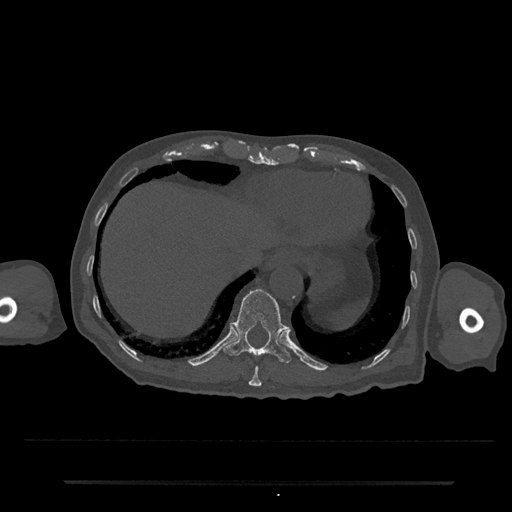
CT including the spine, one axial slice. Slice 265 of 797 in the series (ordered by position). Reconstruction kernel Br40s/3. 120 kVp. Bone window (W 1800 / L 400 HU). 0.5 mm slice thickness. 512 × 512 image matrix, field of view 427 × 427 mm. Male patient, age 74 years. From the clinical record (not read from this slice): primary cancer: prostate.
Annotated regions visible in this slice (semi-automatic segmentation, software-assisted and operator-edited):
- T10 vertebra: bounding box <248,366,262,387> (left, top, right, bottom; pixels)
- T11 vertebra: <224,289,291,363>